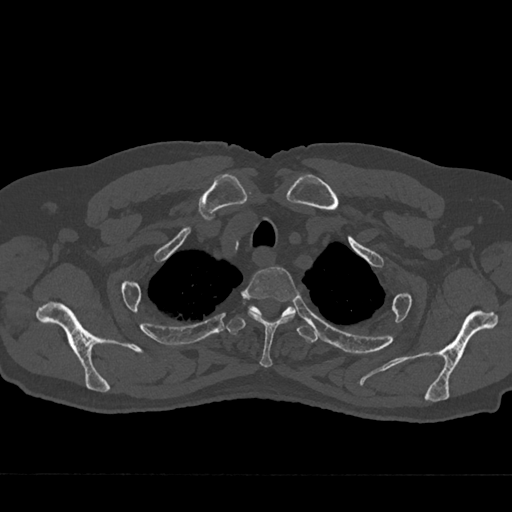
CT including the spine, one axial slice; slice 595 of 797 in the series (ordered by position); reconstruction kernel Br40s/3; 120 kVp; bone window (W 1800 / L 400 HU); 0.5 mm slice thickness; 512 × 512 image matrix, field of view 377 × 377 mm. Male patient, age 75 years. Case-level facts recorded for this patient, not image findings: primary cancer: renal.
Annotated regions visible in this slice (semi-automatic segmentation, software-assisted and operator-edited):
- T2 vertebra: box from (x=242, y=267) to (x=299, y=368) px
- T3 vertebra: (x=226, y=306)–(x=318, y=343)